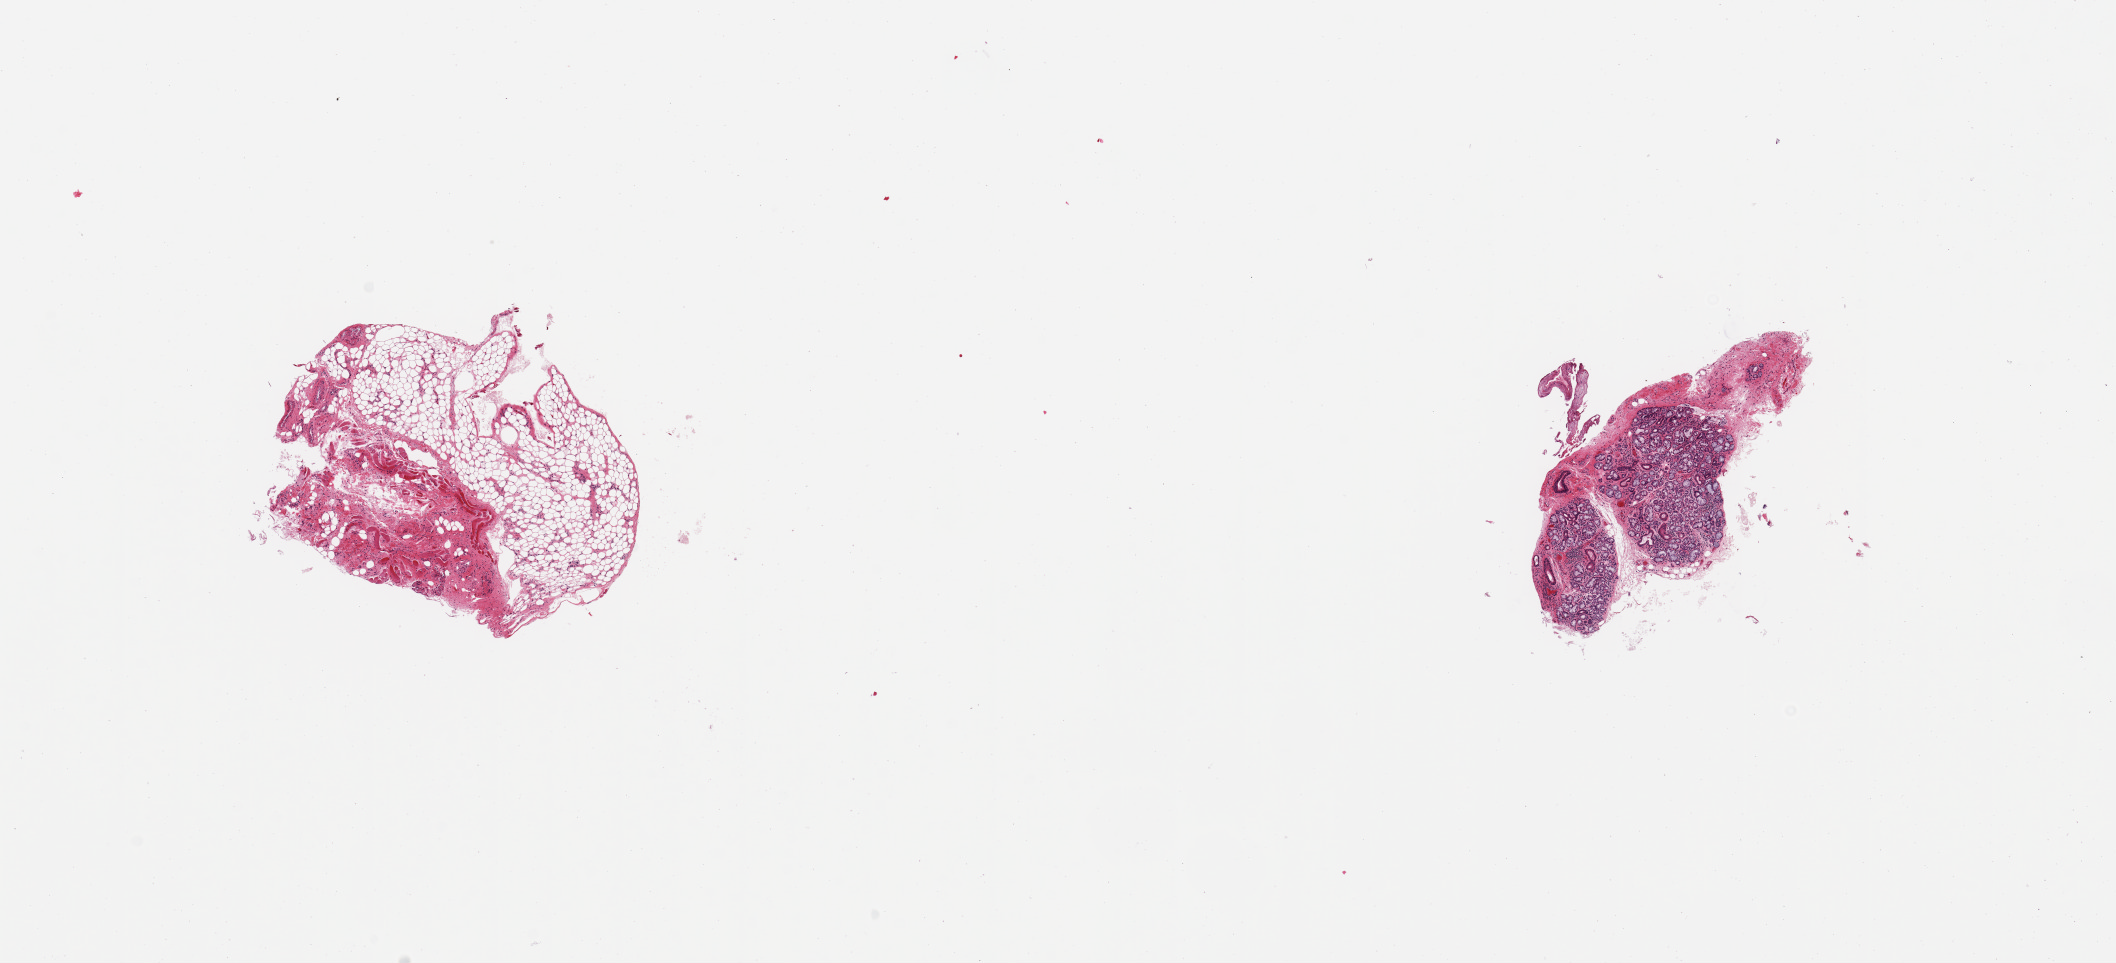
Whole-slide image, hematoxylin and eosin (H&E) stain — a low-resolution overview of the entire scanned area, about 16.7 x 7.6 mm, PAXgene-fixed paraffin-embedded (PFPE) section, target tissue: minor salivary gland, donor tissue sample. Donor: male.
Reviewer comment on this tissue sample: 2 pieces; smaller piece contains slightly inflamed salivary gland and adjacent fibrous stroma; nearby piece of skin; larger piece is fibroadipose & muscular tissue.